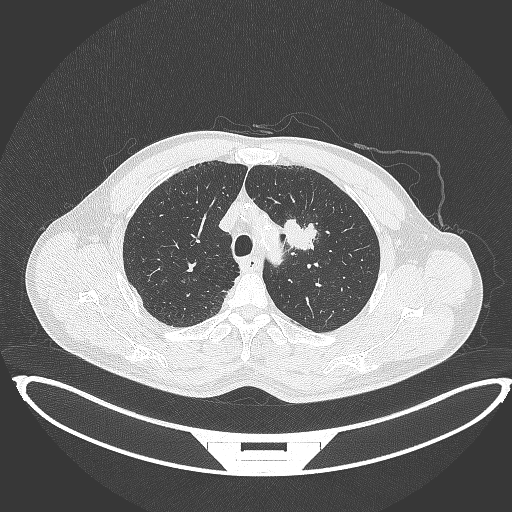
Chest CT, one axial slice. Slice 339 of 395 in the series (ordered by position). Reconstruction kernel B70f. 120 kVp. Lung window (W 1500 / L -600 HU). 512 × 512 image matrix, field of view 457 × 457 mm. Patient: male, 60 years. Case-level facts recorded for this patient, not image findings: clinical TNM (as recorded): T2a N0 M0; histopathological grade: G1-G2.
Outlined on this slice (bounding box drawn by a radiologist):
- lung tumour (recorded histology: squamous cell carcinoma): box from (x=279, y=213) to (x=322, y=253) px